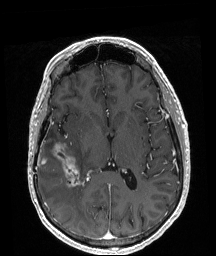
Brain MRI from a brain-tumour surgery series, one axial slice; position 100 of 208 along the scan axis; T1-weighted post-contrast; 1 mm slice thickness; 216 × 256 image matrix, field of view 211 × 250 mm. Case-level facts recorded for this patient, not image findings: histopathology: Astrocytoma; WHO grade: 4; IDH mutation: yes.
Outlined on this slice (outlined manually by an expert reader):
- tumour: bounding box (x1, y1, x2, y2) in pixels: (38, 143, 80, 187)